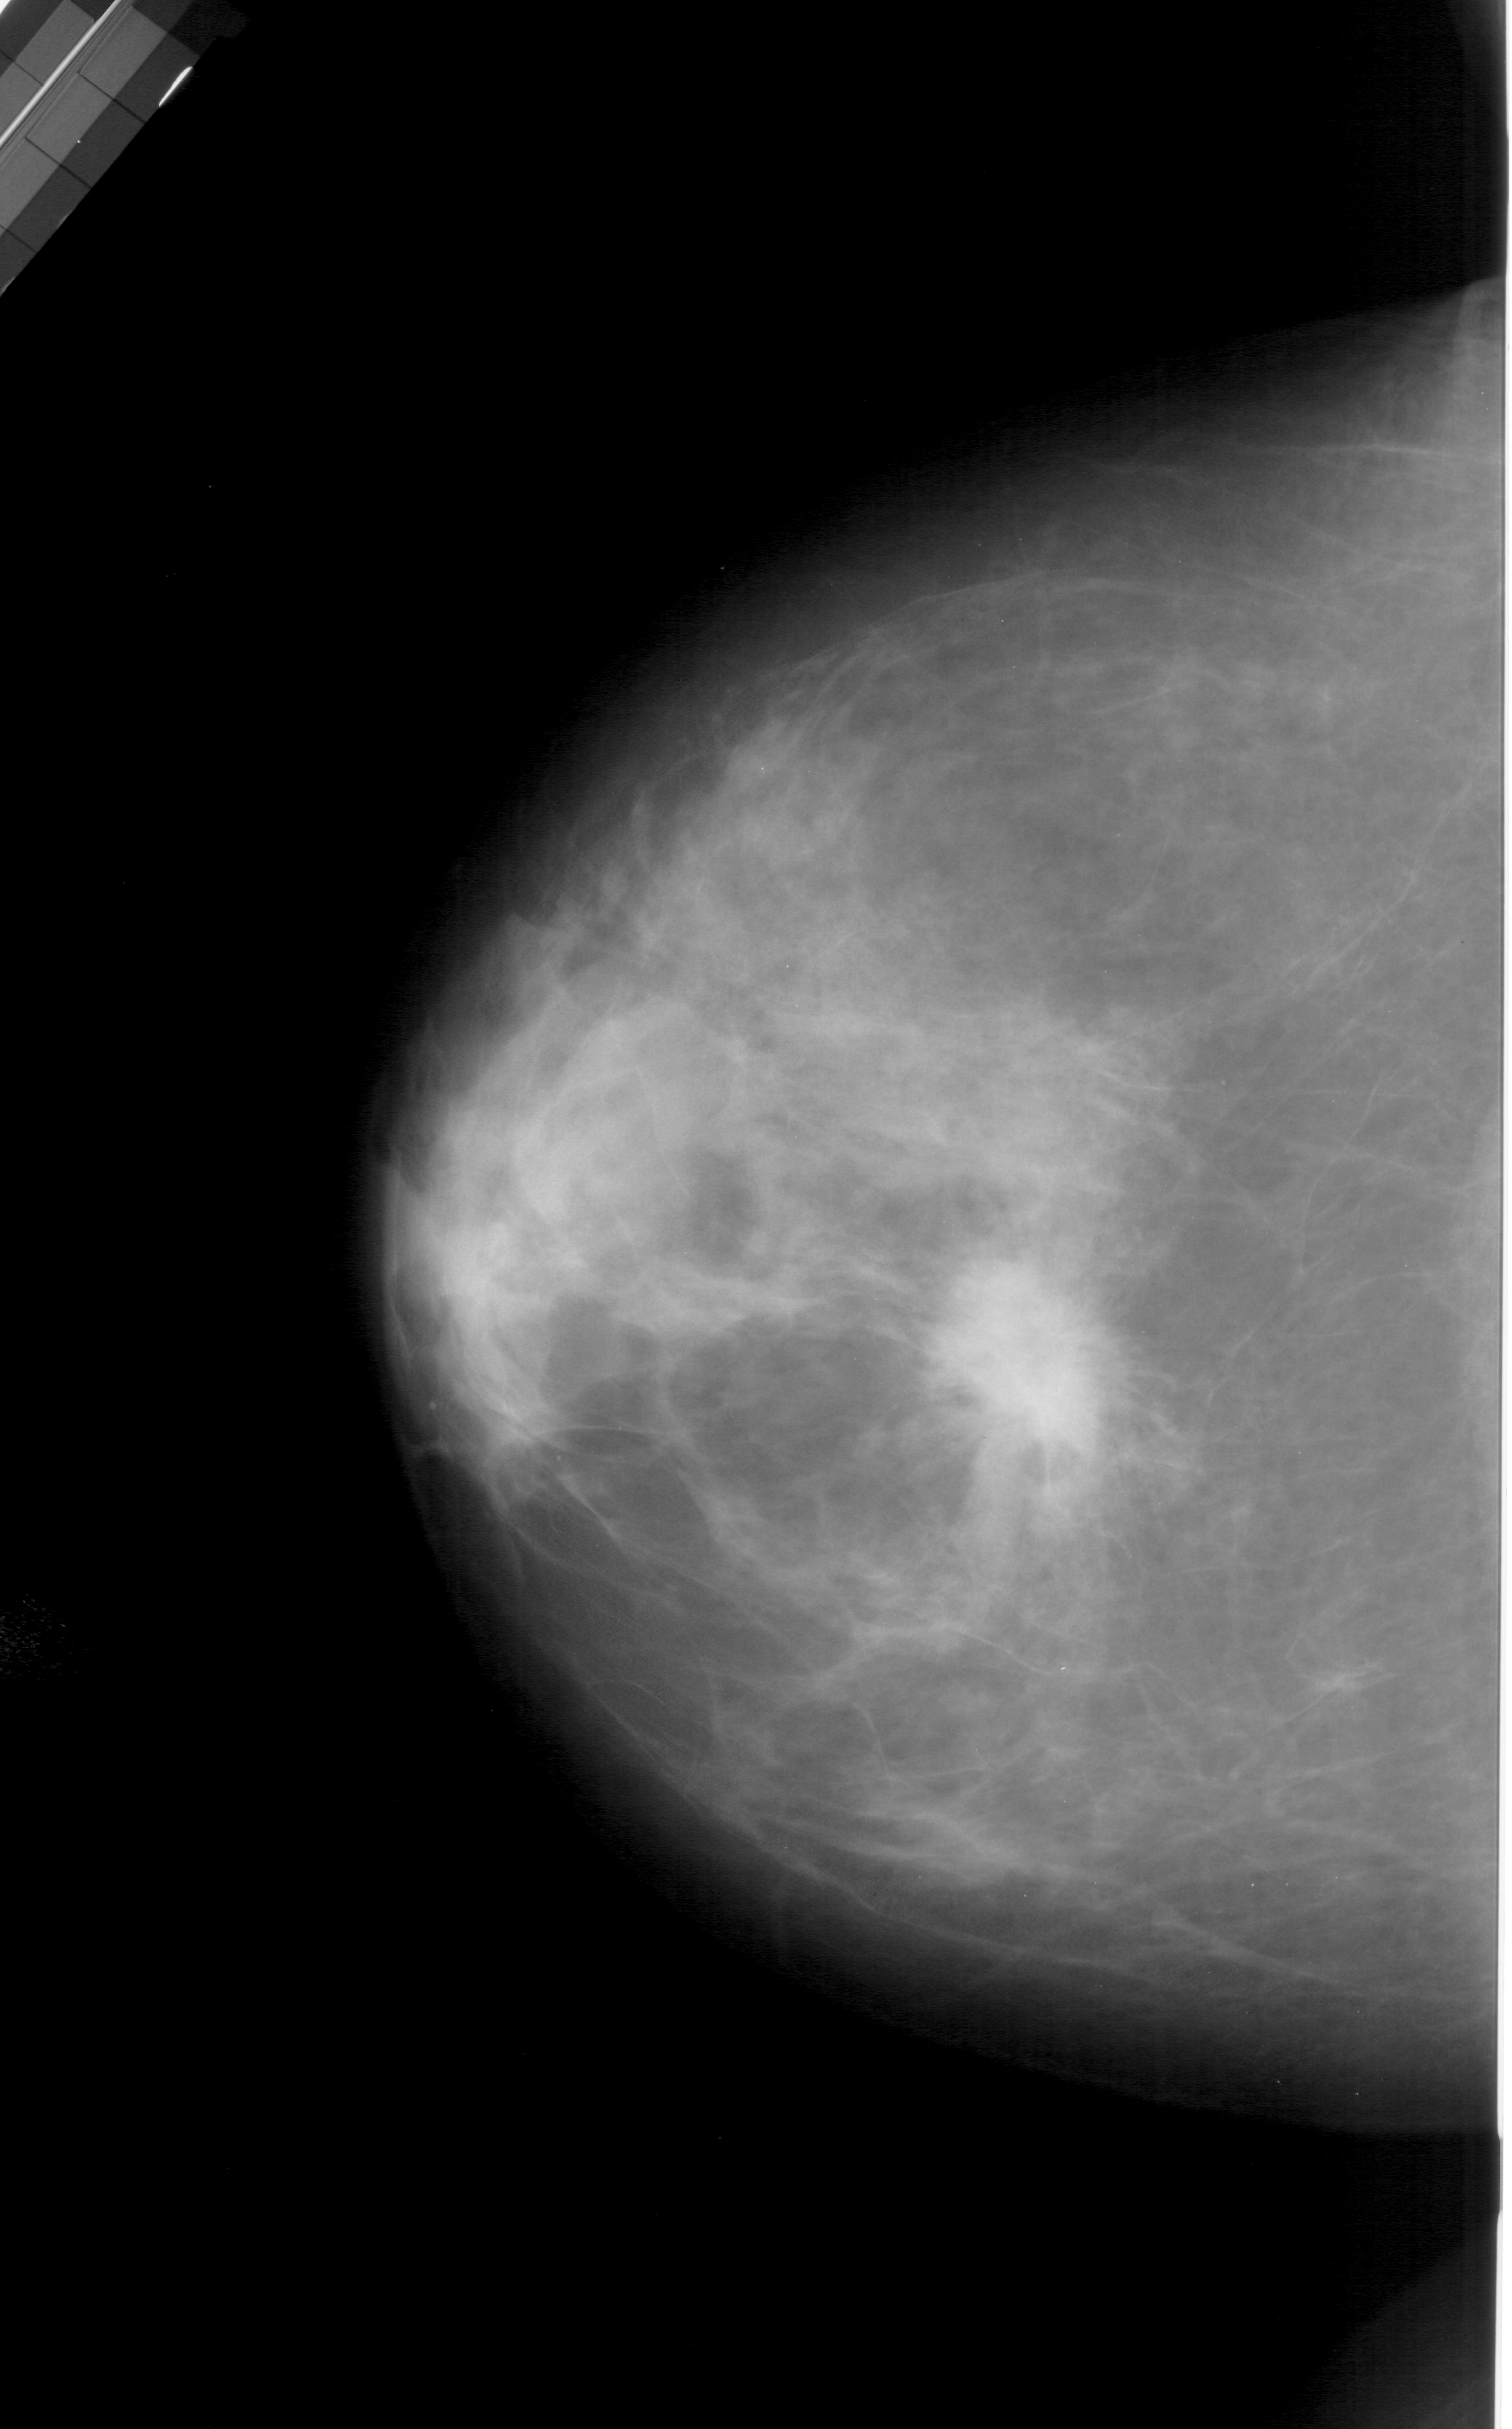
Mammogram (digitized film); left breast; craniocaudal (CC) view; breast composition: heterogeneously dense (BI-RADS density category 3 of 4).
- Abnormality record for this image: mass, shape irregular, margins spiculated; BI-RADS assessment category 5; pathology result (as recorded, not read from the image): malignant.